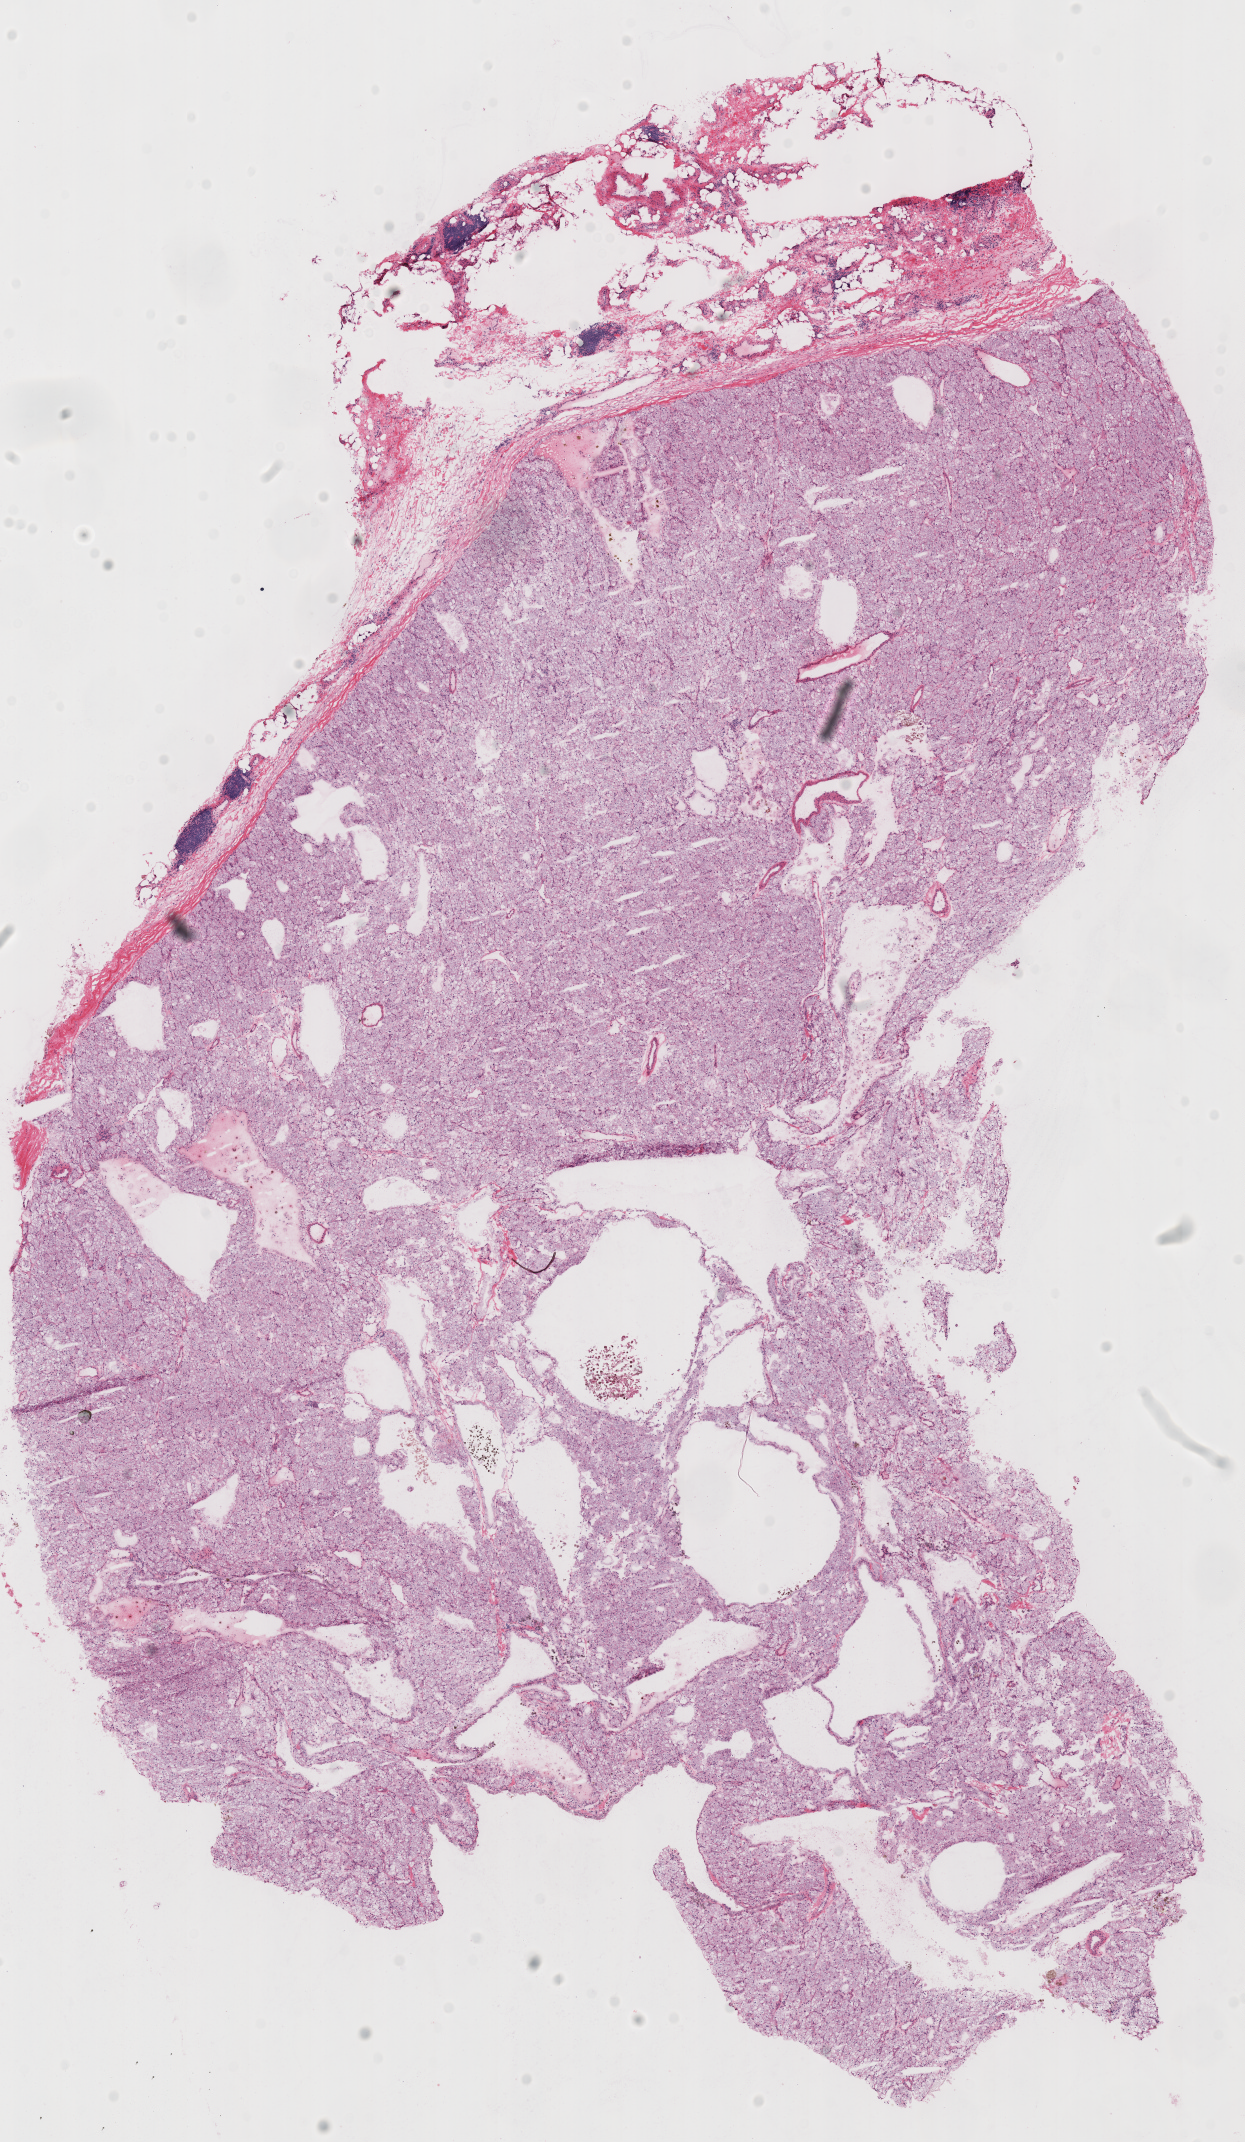
Whole-slide histology image, Hematoxylin and eosin (H&E) stained, a low-resolution overview of the entire scanned area, about 9.8 x 16.8 mm (from a 40x scan); frozen section from the top of the tissue portion; sample: primary tumour, kidney. Patient: male, age at initial diagnosis 69 years.
Diagnosis: Renal cell carcinoma, chromophobe type.